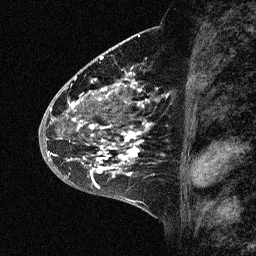
Breast MRI (dynamic contrast-enhanced), one sagittal slice; slice 27 of 64 in the series (ordered by position); dynamic contrast-enhanced study with each time point stored as its own series, time point 2 of 3 at this slice position (early post-contrast, ordered by acquisition time); 1.5 T; TE 4.5 ms, TR 11 ms; 2.06 mm slice thickness; 256 × 256 image matrix, field of view 200 × 200 mm. Patient: female, 46 years. Case-level facts recorded for this patient, not image findings: setting: breast cancer imaged before/during neoadjuvant chemotherapy; receptor status: HER2-positive.
Outlined on this slice (semi-automatic segmentation, software-assisted and operator-edited):
- analysis volume of interest (the breast-tissue region the enhancement analysis was run in; not a lesion): bounding box <43,72,176,177> (left, top, right, bottom; pixels)
- tumour enhancement mask (voxels above the 90 % enhancement threshold inside the analysis volume of interest): <48,72,155,177>